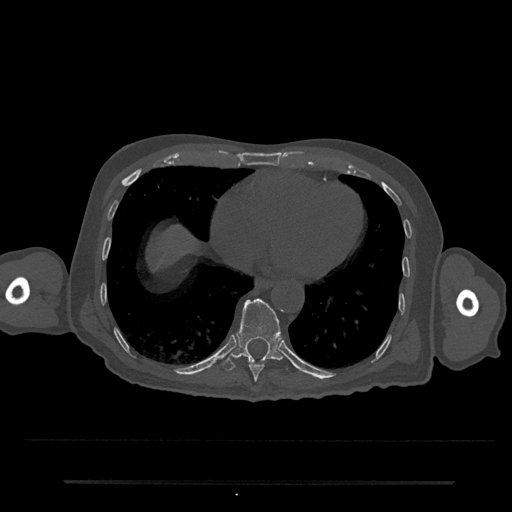
CT including the spine, one axial slice; slice 334 of 797 in the series (ordered by position); bone window (W 1800 / L 400 HU); 512 × 512 image matrix, field of view 427 × 427 mm. Male patient, age 74 years. Case-level facts recorded for this patient, not image findings: primary cancer: prostate.
Outlined on this slice (semi-automatically segmented with operator editing):
- T10 vertebra: bounding box (x1, y1, x2, y2) in pixels: (222, 298, 283, 371)
- T9 vertebra: (249, 361, 265, 382)